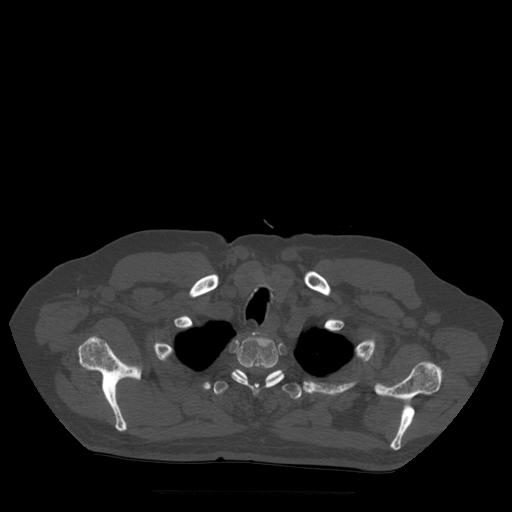
CT including the spine, one axial slice; slice 421 of 522 in the series (ordered by position); bone window (W 1800 / L 400 HU); 1.25 mm slice thickness; 512 × 512 image matrix, field of view 420 × 420 mm. Patient age 72 years. From the clinical record (not read from this slice): primary cancer: prostate.
Structures marked on this image (semi-automatic segmentation, software-assisted and operator-edited):
- T1 vertebra: box from (x=253, y=333) to (x=256, y=335) px
- T2 vertebra: (x=232, y=336)–(x=284, y=390)
- T3 vertebra: (x=214, y=369)–(x=303, y=400)